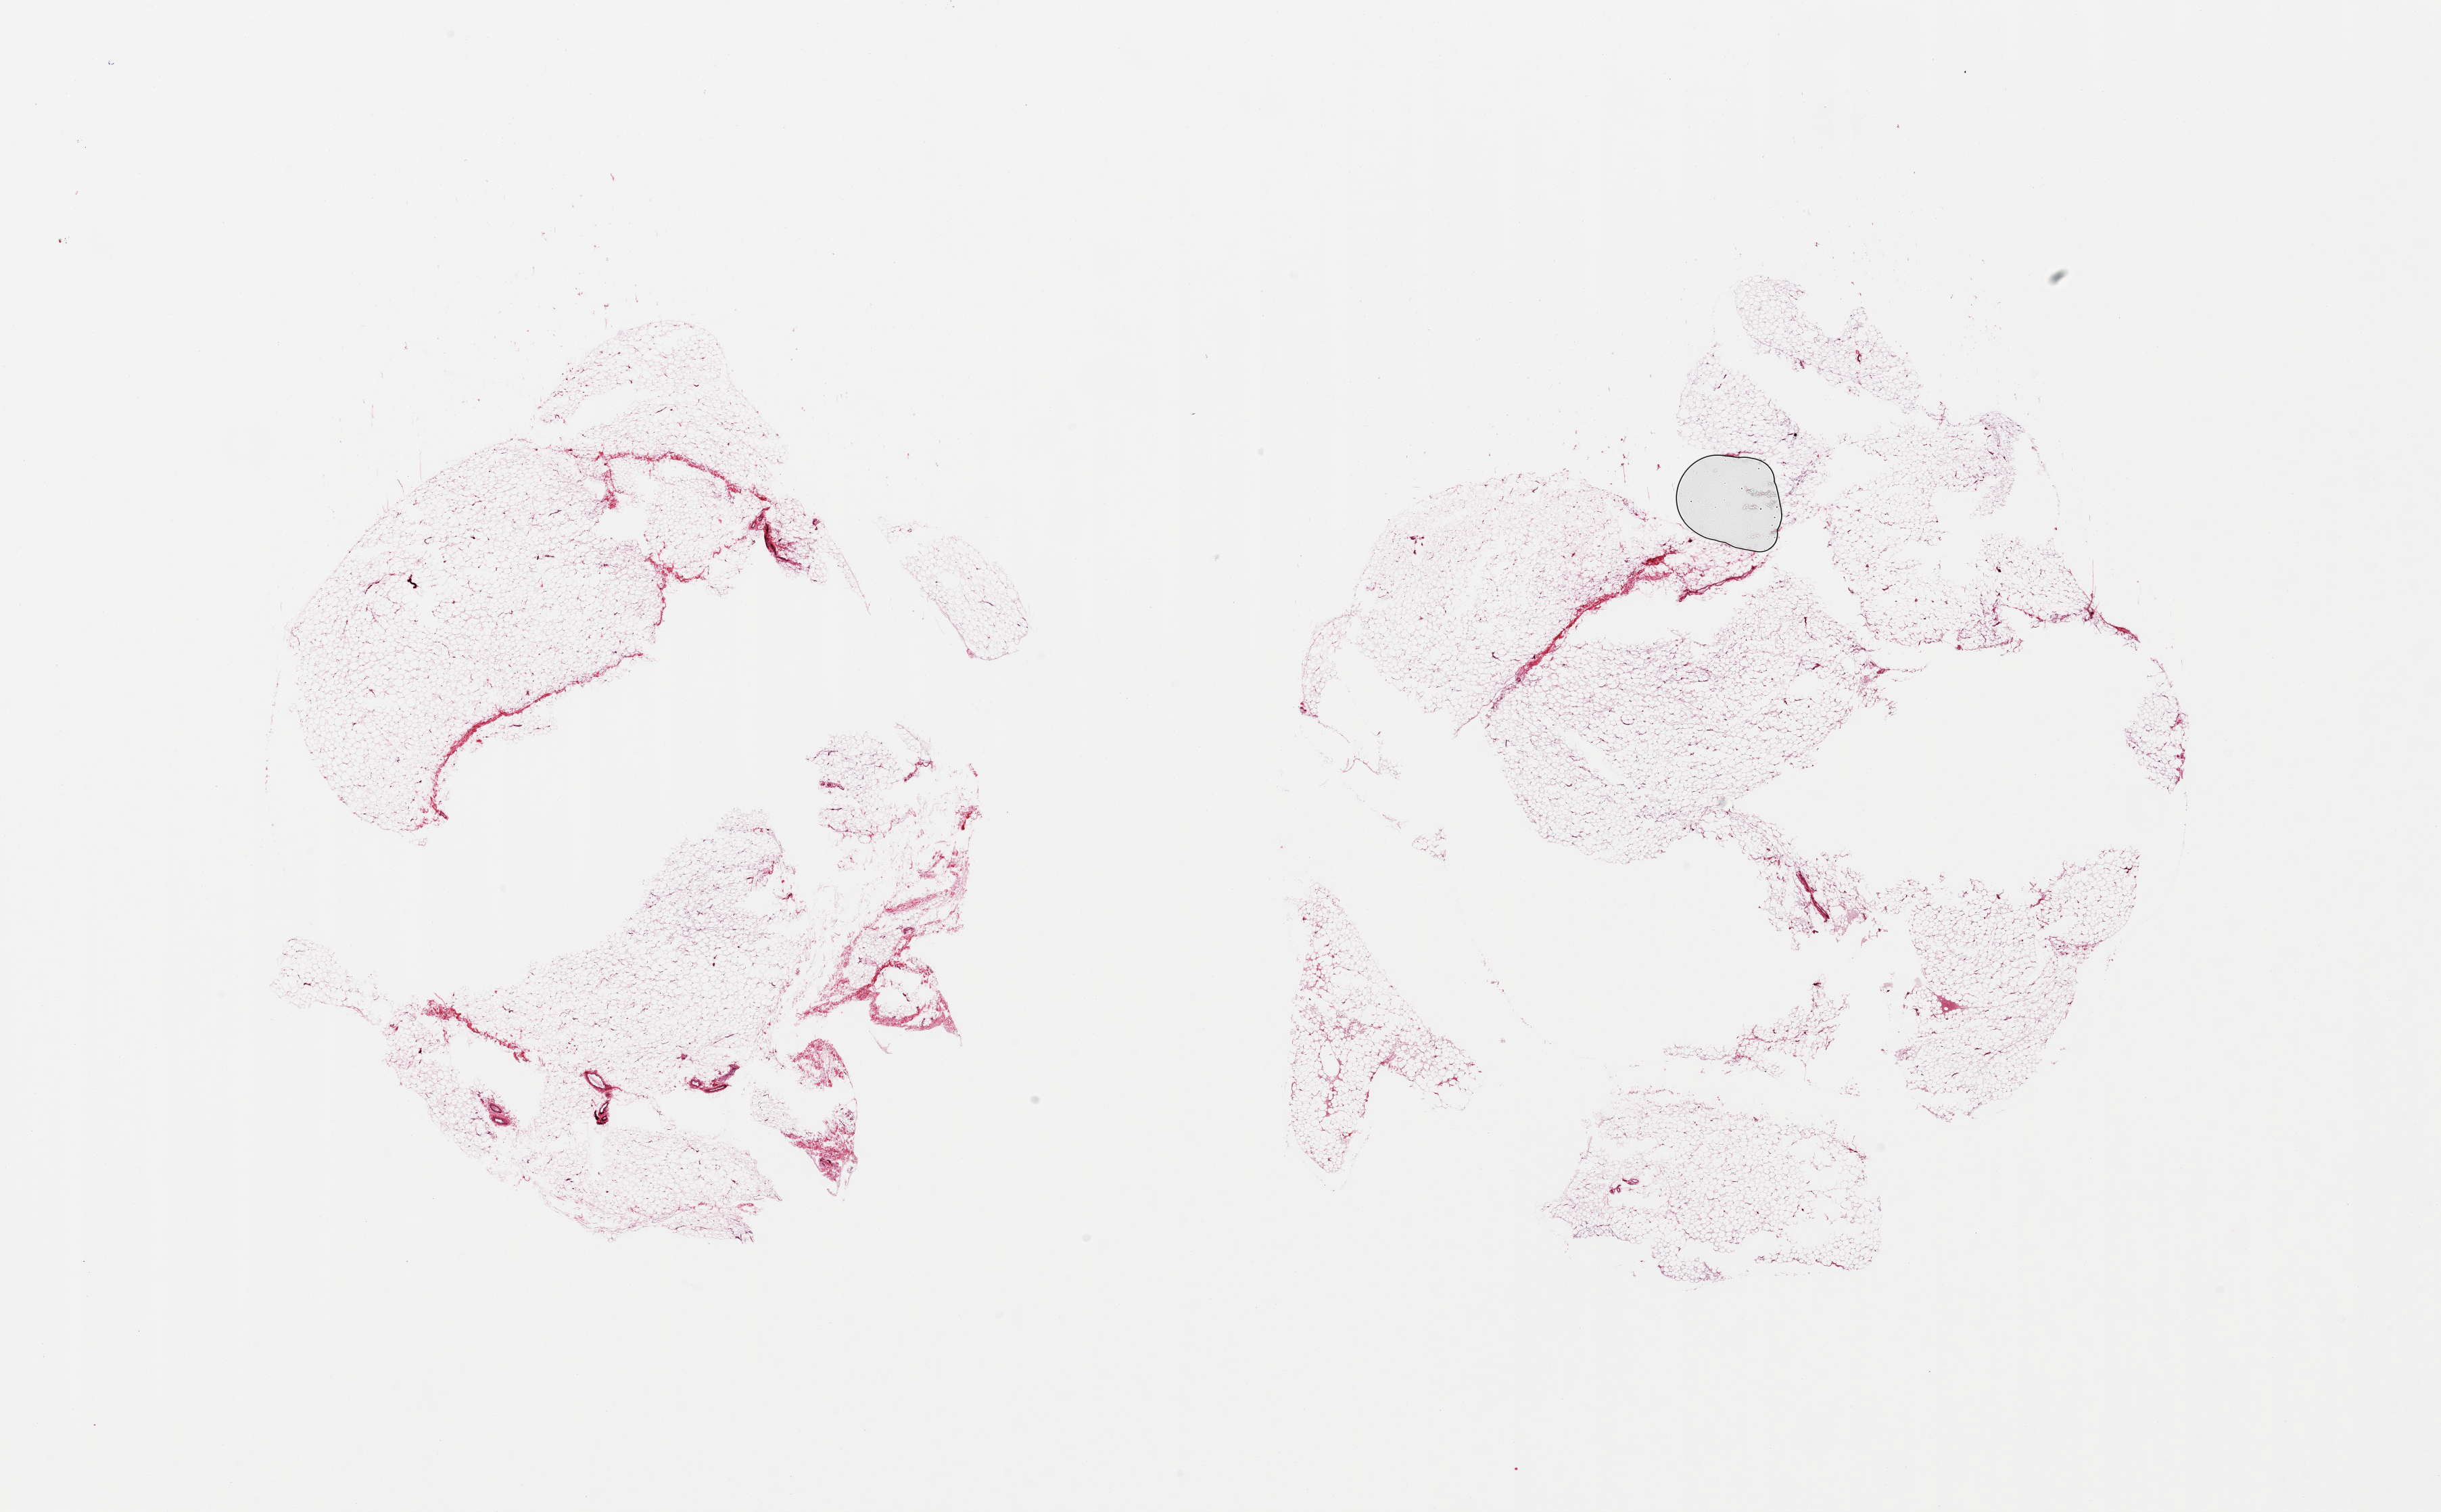
Hematoxylin and eosin (H&E) whole-slide image — low-resolution overview of the scanned area, about 28.5 x 17.7 mm. PAXgene-fixed, paraffin-embedded tissue. Section of adipose tissue (target tissue). Donor tissue sample. Donor: male.
* reviewer comment on this tissue sample: 2 pieces; <5% fibrous content; several holes in tissue